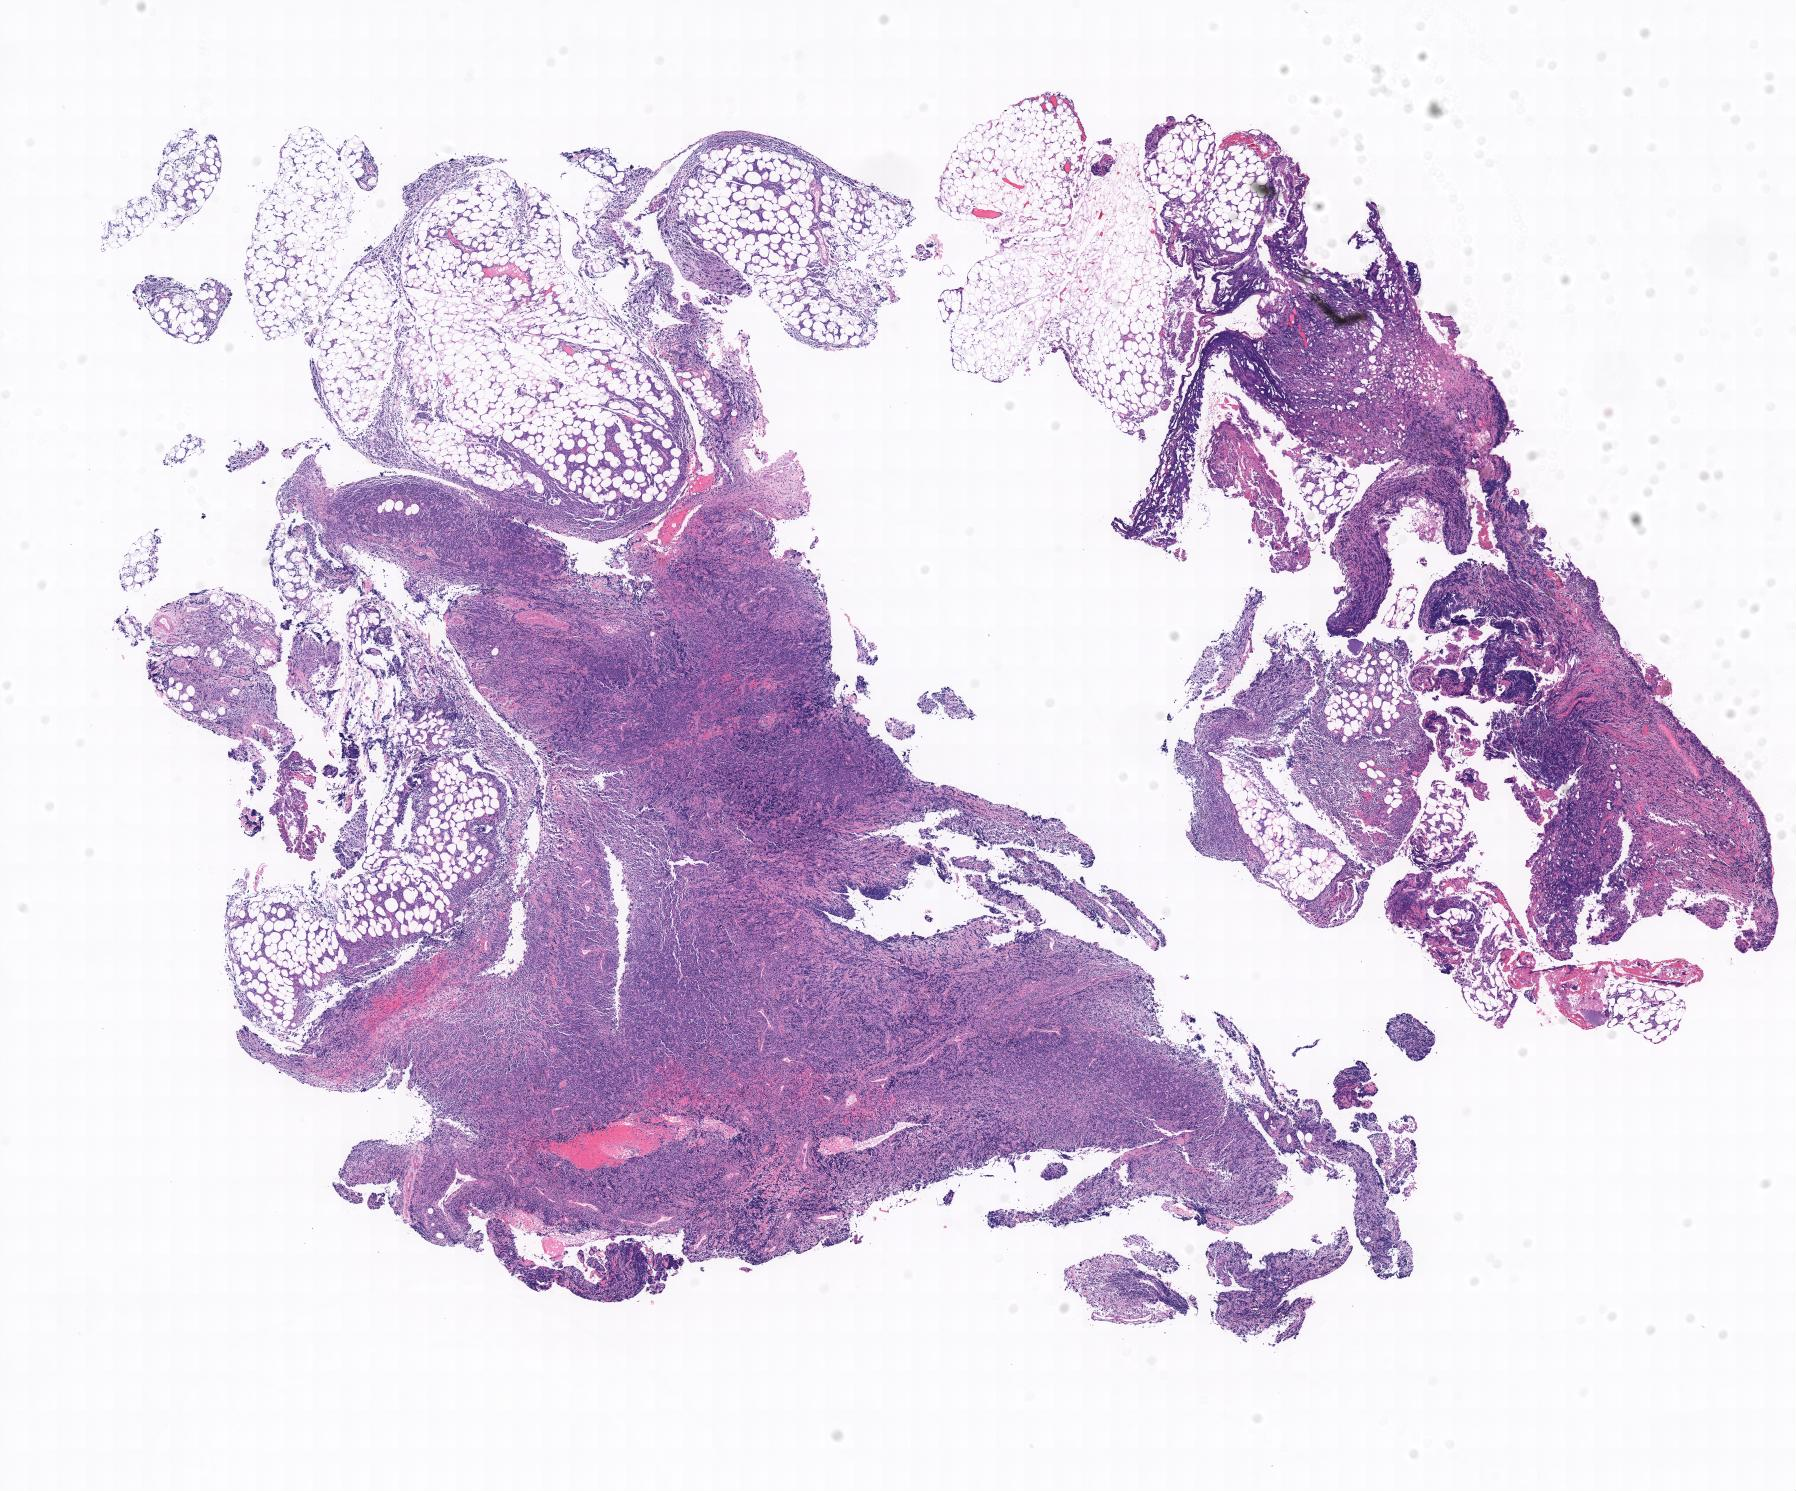
Digitized haematoxylin and eosin-stained section, shown as a low-resolution overview of the whole scanned area. Specimen: tumor tissue. Anatomic site: abdominal lymph node. Male patient; age at initial diagnosis 9 years.
• diagnosis: Burkitt lymphoma, NOS